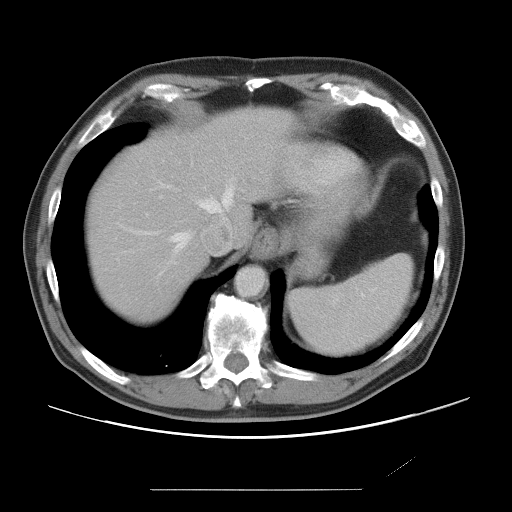
Contrast-enhanced abdominal CT, one axial slice; soft-tissue window (W 400 / L 40 HU); 5 mm slice thickness; 512 × 512 image matrix. Male patient, age 74 years. From the clinical record (not read from this slice): diagnosis: colorectal cancer liver metastases, imaged before liver resection; multiple liver metastases: yes; largest metastasis: 1.1 cm; disease in both lobes: no.
Structures marked on this image (manually delineated by an expert):
- hepatic veins: bounding box <136,183,233,251> (left, top, right, bottom; pixels)
- liver: <86,109,293,318>
- planned liver remnant (the part of the liver to remain after resection): <86,109,293,318>